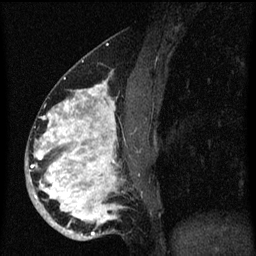
Breast MRI (dynamic contrast-enhanced), one sagittal slice; position 28 of 60 along the scan axis; dynamic contrast-enhanced series, image 2 of 3 at this slice position (ordered by acquisition); 1.5 T; TE 4.2 ms, TR 8.4 ms; 256 × 256 image matrix, field of view 180 × 180 mm. Patient: female, 34 years. From the clinical record (not read from this slice): setting: breast cancer imaged before/during neoadjuvant chemotherapy; receptor status: HR-positive, HER2-negative.
Structures marked on this image (semi-automatic segmentation, software-assisted and operator-edited):
- analysis volume of interest (the breast-tissue region the enhancement analysis was run in; not a lesion): box from (x=26, y=58) to (x=139, y=241) px
- tumour enhancement mask (voxels above the 70 % enhancement threshold inside the analysis volume of interest): (x=30, y=80)–(x=123, y=237)